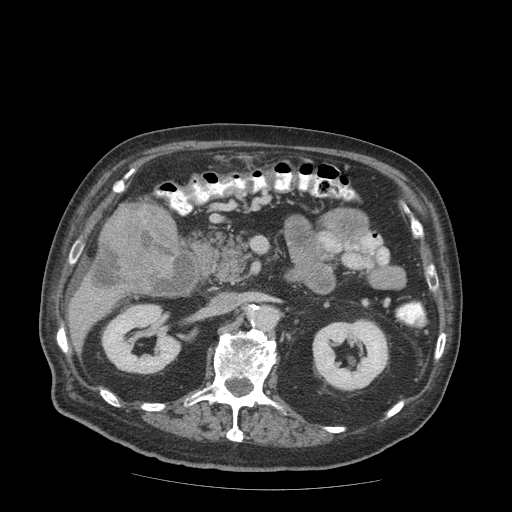
Contrast-enhanced abdominal CT (liver protocol), one axial slice. Slice 29 of 99 in the series (ordered by position). Soft-tissue window (W 400 / L 40 HU). 2.5 mm slice thickness. 512 × 512 image matrix, field of view 420 × 420 mm. Case-level facts recorded for this patient, not image findings: diagnosis: hepatocellular carcinoma (patient treated with transarterial chemoembolisation; whether this scan precedes or follows treatment is not stated here); TNM stage (as recorded): Stage-IIIB.
Structures marked on this image (semi-automatically segmented with operator editing):
- liver parenchyma outside the tumour (the mass and vessels are separate outlines, so this box may not span the whole liver): bounding box (x1, y1, x2, y2) in pixels: (68, 202, 184, 349)
- mass: (91, 201, 181, 292)